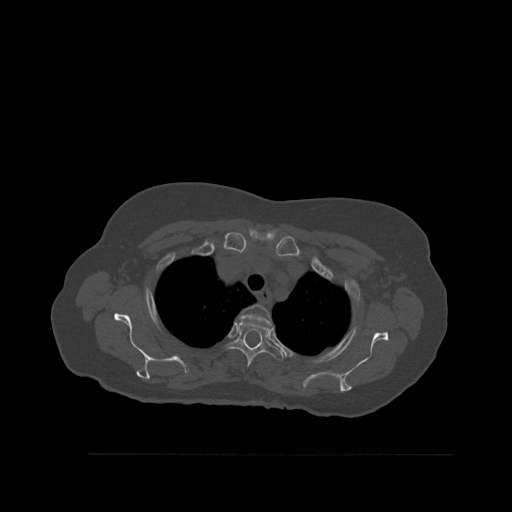
CT including the spine, one axial slice. Bone window (W 1800 / L 400 HU). 1.5 mm slice thickness. 512 × 512 image matrix, field of view 470 × 470 mm. Female patient, age 73 years. From the clinical record (not read from this slice): primary cancer: breast; vertebrae with lytic lesions (as recorded): L2.
Annotated regions visible in this slice (semi-automatic segmentation, software-assisted and operator-edited):
- T2 vertebra: bounding box [x1, y1, x2, y2] px = [239, 305, 273, 328]
- T3 vertebra: [223, 320, 284, 369]